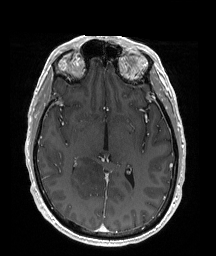
Brain MRI from a brain-tumour surgery series, one axial slice. Position 100 of 176 along the scan axis. T1-weighted post-contrast. 1 mm slice thickness. 216 × 256 image matrix, field of view 211 × 250 mm. From the clinical record (not read from this slice): histopathology: Oligodendroglioma; WHO grade: 2; IDH mutation: yes; tumour location: Right Parietal.
Structures marked on this image (outlined manually by an expert reader):
- tumour: bounding box <70,155,111,194> (left, top, right, bottom; pixels)